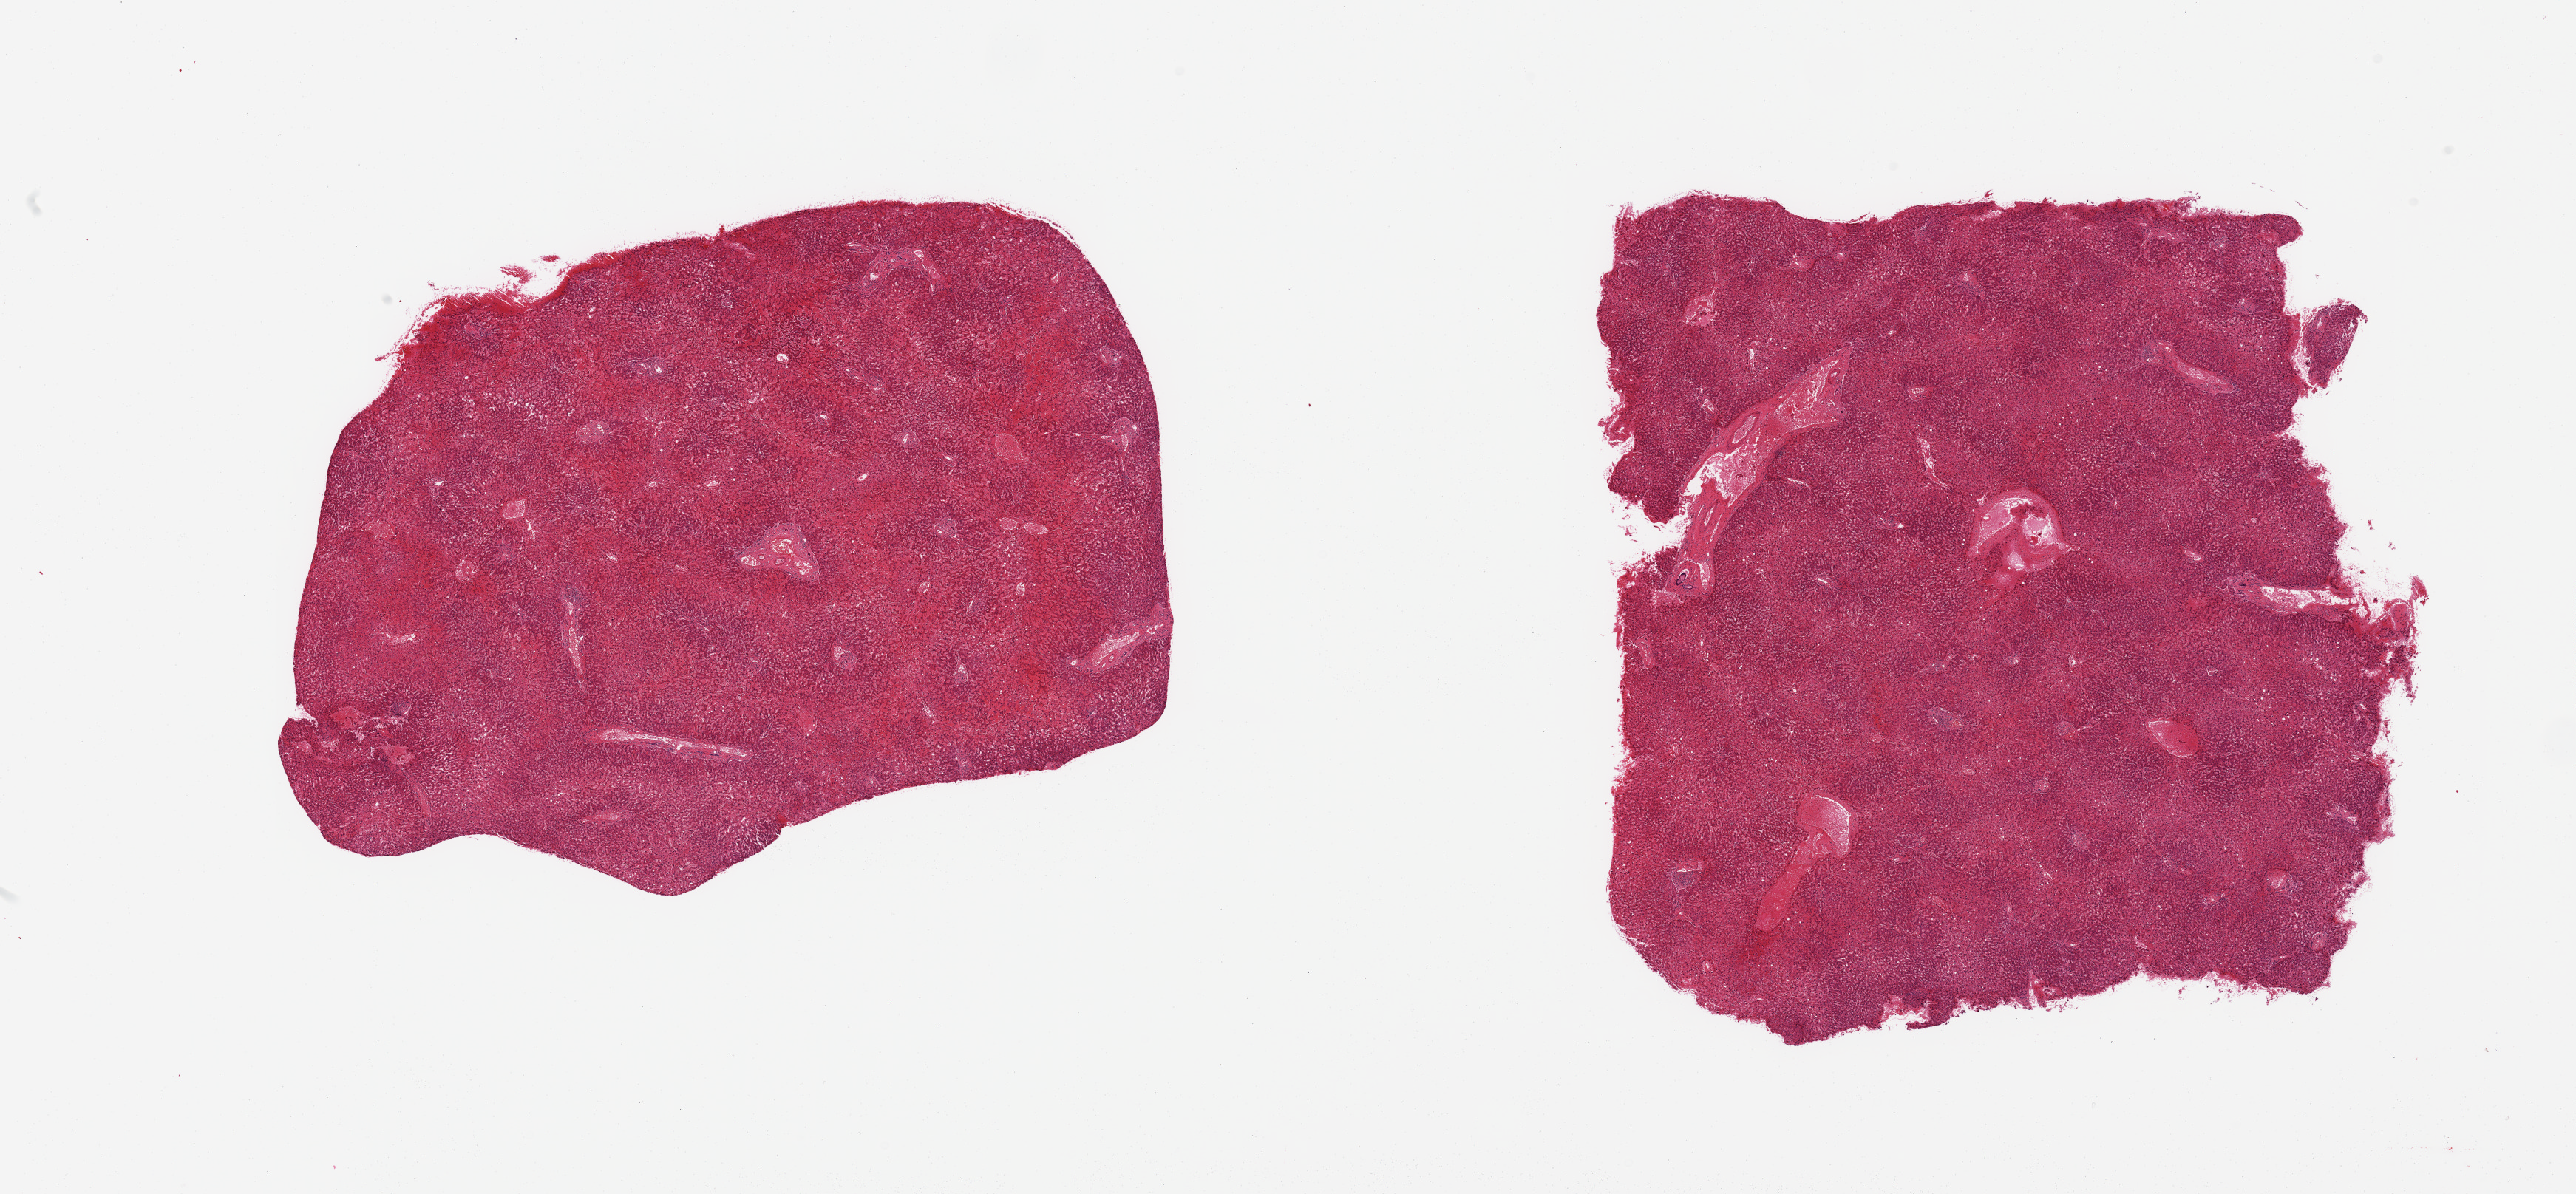
Whole-slide image, hematoxylin and eosin (H&E) stain, shown as a low-resolution overview of the whole scanned area (about 27.6 x 12.8 mm); PAXgene-fixed, paraffin-embedded tissue; target tissue: liver; donor tissue sample. Donor sex: male.
• reviewer comment on this tissue sample: 2 pieces; marked congestion